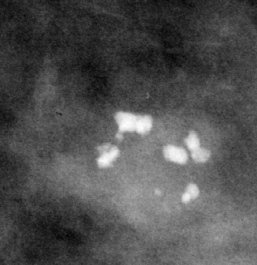
Region of interest cut from a scanned film mammogram (one marked finding); left breast; MLO view; BI-RADS breast density category 3 (scale 1–4).
Calcifications, morphology dystrophic, distribution clustered; BI-RADS assessment category 2; subtlety rating 5 on a 1 (subtle) to 5 (obvious) scale; benign without callback (not worked up further).